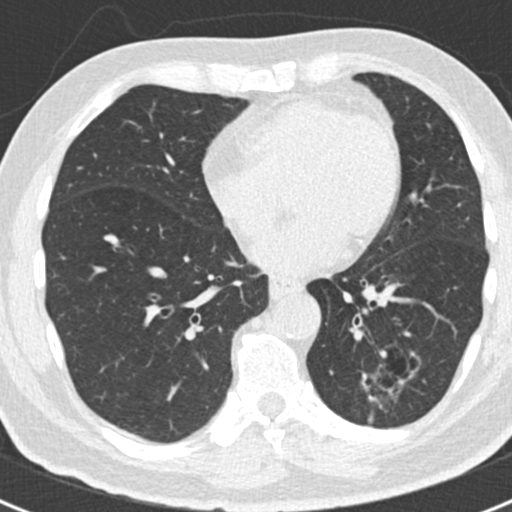
Chest CT (low-dose screening protocol), one axial image. First (baseline) screen. Lung window (W 1500 / L -600 HU). 2 mm slice thickness. Slice 103 of 188 in the series. 512 × 512 image matrix. Male, age 66 years at enrolment. Former smoker at enrolment.
• Expert reader's lesion annotation, bounding box <342,337,420,415> (left, top, right, bottom; pixels).
• Screening reader's record for this exam (one nodule recorded; not confirmed to be the boxed lesion): non-calcified nodule or mass ≥4 mm, left lower lobe, 43 × 27 mm, smooth margins.
• Later outcome: lung cancer diagnosed 801 days after this screen (after the third annual screen) — adenocarcinoma, NOS, left lower lobe, poorly differentiated (G3), stage IB (AJCC 6th edition), 38 mm at pathology.